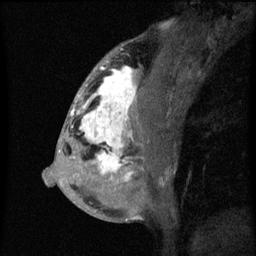
Breast MRI (dynamic contrast-enhanced), one sagittal slice. Position 30 of 60 along the scan axis. Dynamic contrast-enhanced series, image 2 of 3 at this slice position (ordered by acquisition). 1.5 T. TE 4.2 ms, TR 8 ms. 2 mm slice thickness. 256 × 256 image matrix. Female patient, age 50 years.
Structures marked on this image (semi-automatic segmentation, software-assisted and operator-edited):
- analysis volume of interest (the breast-tissue region the enhancement analysis was run in; not a lesion): bounding box [x1, y1, x2, y2] px = [66, 64, 141, 187]
- tumour enhancement mask (voxels above the 70 % enhancement threshold inside the analysis volume of interest): [70, 66, 137, 181]